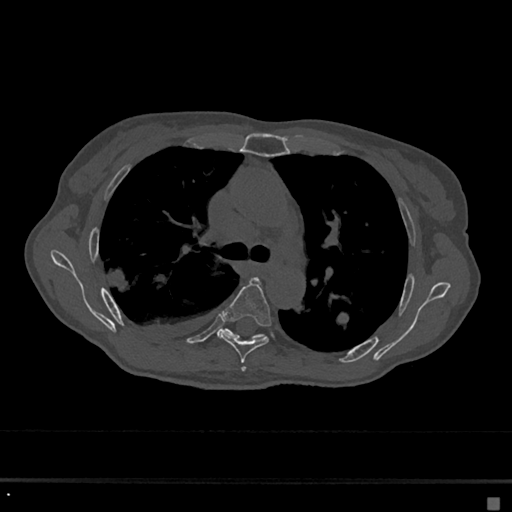
CT including the spine, one axial slice; position 453 of 797 along the scan axis; reconstruction kernel Br40s/3; 120 kVp; bone window (W 1800 / L 400 HU); 512 × 512 image matrix. Patient: female, 68 years. Case-level facts recorded for this patient, not image findings: primary cancer: renal.
Structures marked on this image (semi-automatically segmented with operator editing):
- T4 vertebra: bounding box [x1, y1, x2, y2] px = [242, 367, 245, 371]
- T5 vertebra: [219, 278, 272, 364]
- T6 vertebra: [217, 328, 265, 340]